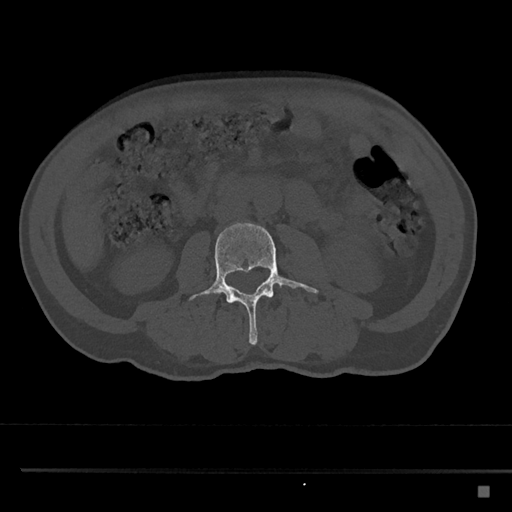
CT including the spine, one axial slice. Slice 695 of 797 in the series (ordered by position). Reconstruction kernel Br40s/3. 120 kVp. Bone window (W 1800 / L 400 HU). 0.5 mm slice thickness. 512 × 512 image matrix. Patient: male, 59 years. Case-level facts recorded for this patient, not image findings: primary cancer: prostate.
Outlined on this slice (semi-automatically segmented with operator editing):
- L3 vertebra: bounding box <190,223,318,345> (left, top, right, bottom; pixels)